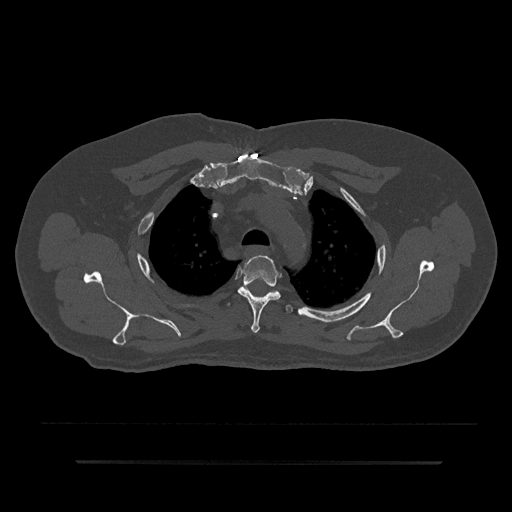
CT including the spine, one axial slice. Slice 652 of 797 in the series (ordered by position). Reconstruction kernel Br40s/3. 120 kVp. Bone window (W 1800 / L 400 HU). 0.5 mm slice thickness. 512 × 512 image matrix, field of view 464 × 464 mm. Male patient, age 59 years. From the clinical record (not read from this slice): primary cancer: bile ducts; vertebrae with lytic lesions (as recorded): T10.
Structures marked on this image (semi-automatic segmentation, software-assisted and operator-edited):
- T3 vertebra: bounding box <238,255,281,333> (left, top, right, bottom; pixels)
- T4 vertebra: <226,303,293,312>